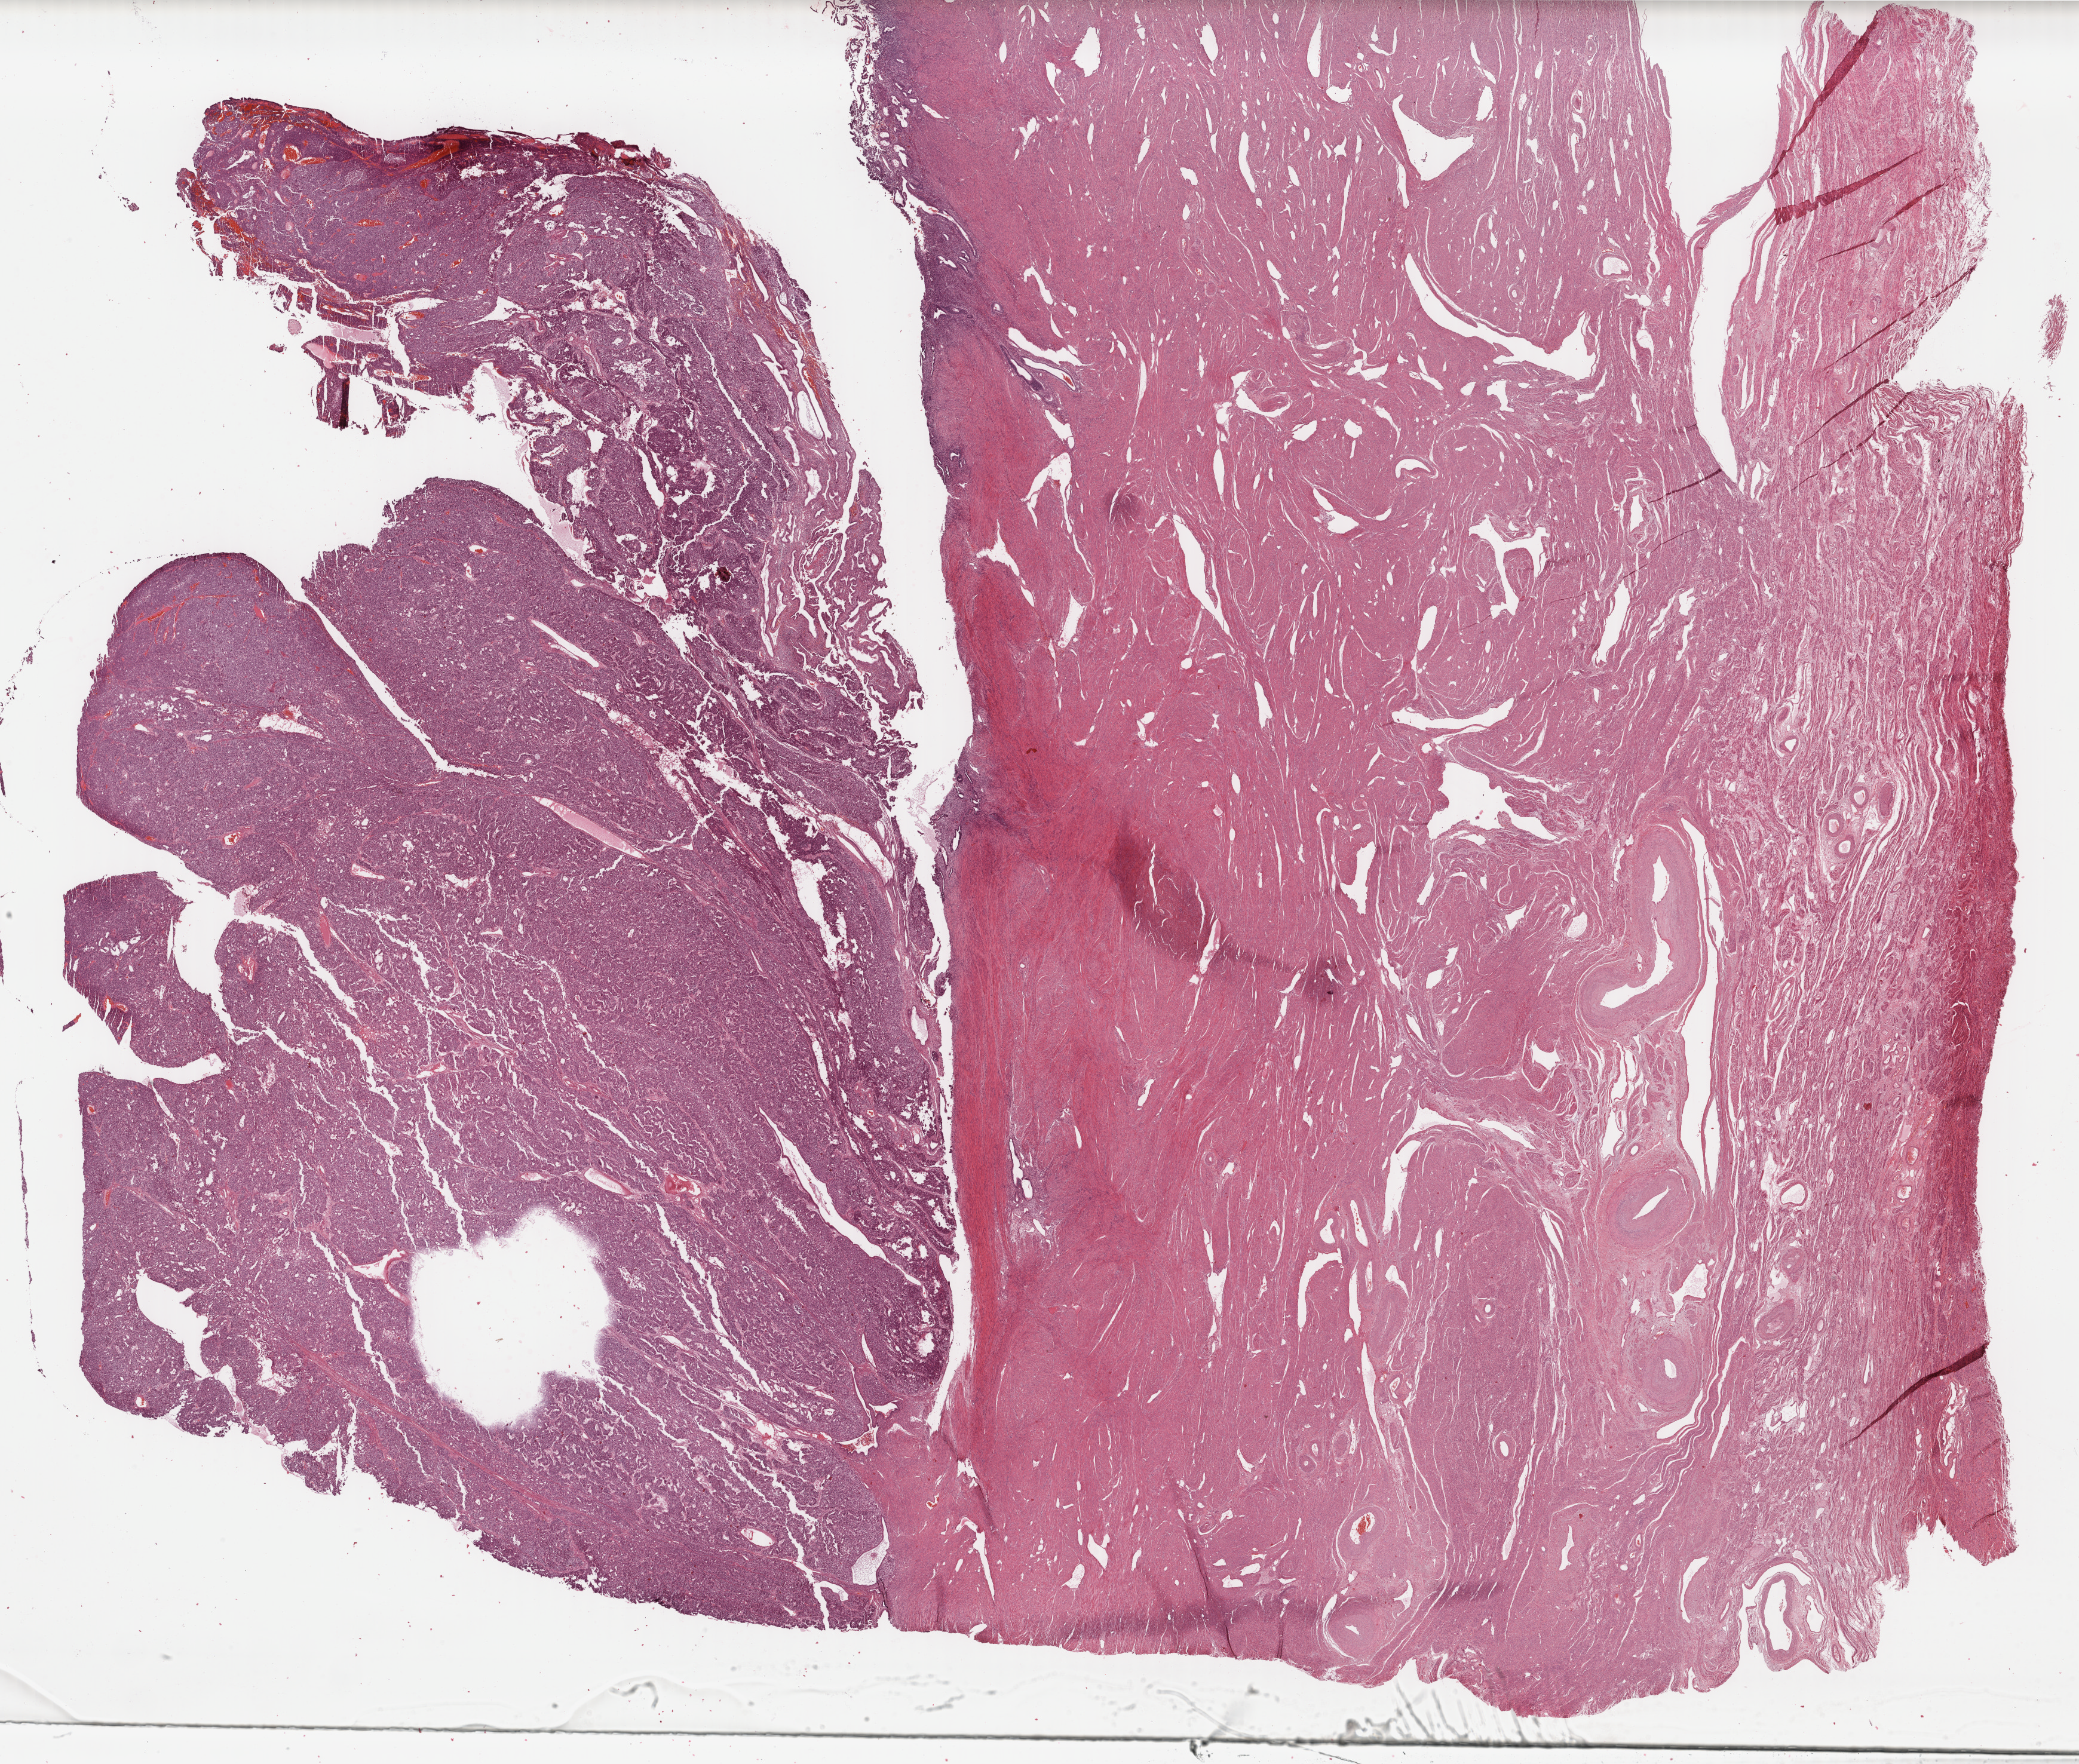
Digitized H&E tissue section (whole slide) — shown as a low-resolution overview of the whole scanned area (about 27.6 x 23.4 mm); FFPE section; sample: primary tumour, uterus. Female, age 59 years at initial diagnosis. Histologic grade: G3 (poorly differentiated).
* histologic diagnosis: Endometrioid adenocarcinoma, NOS (endometrium)
* FIGO stage: IIA
* lymph nodes positive (case pathology): 0 of 34 examined